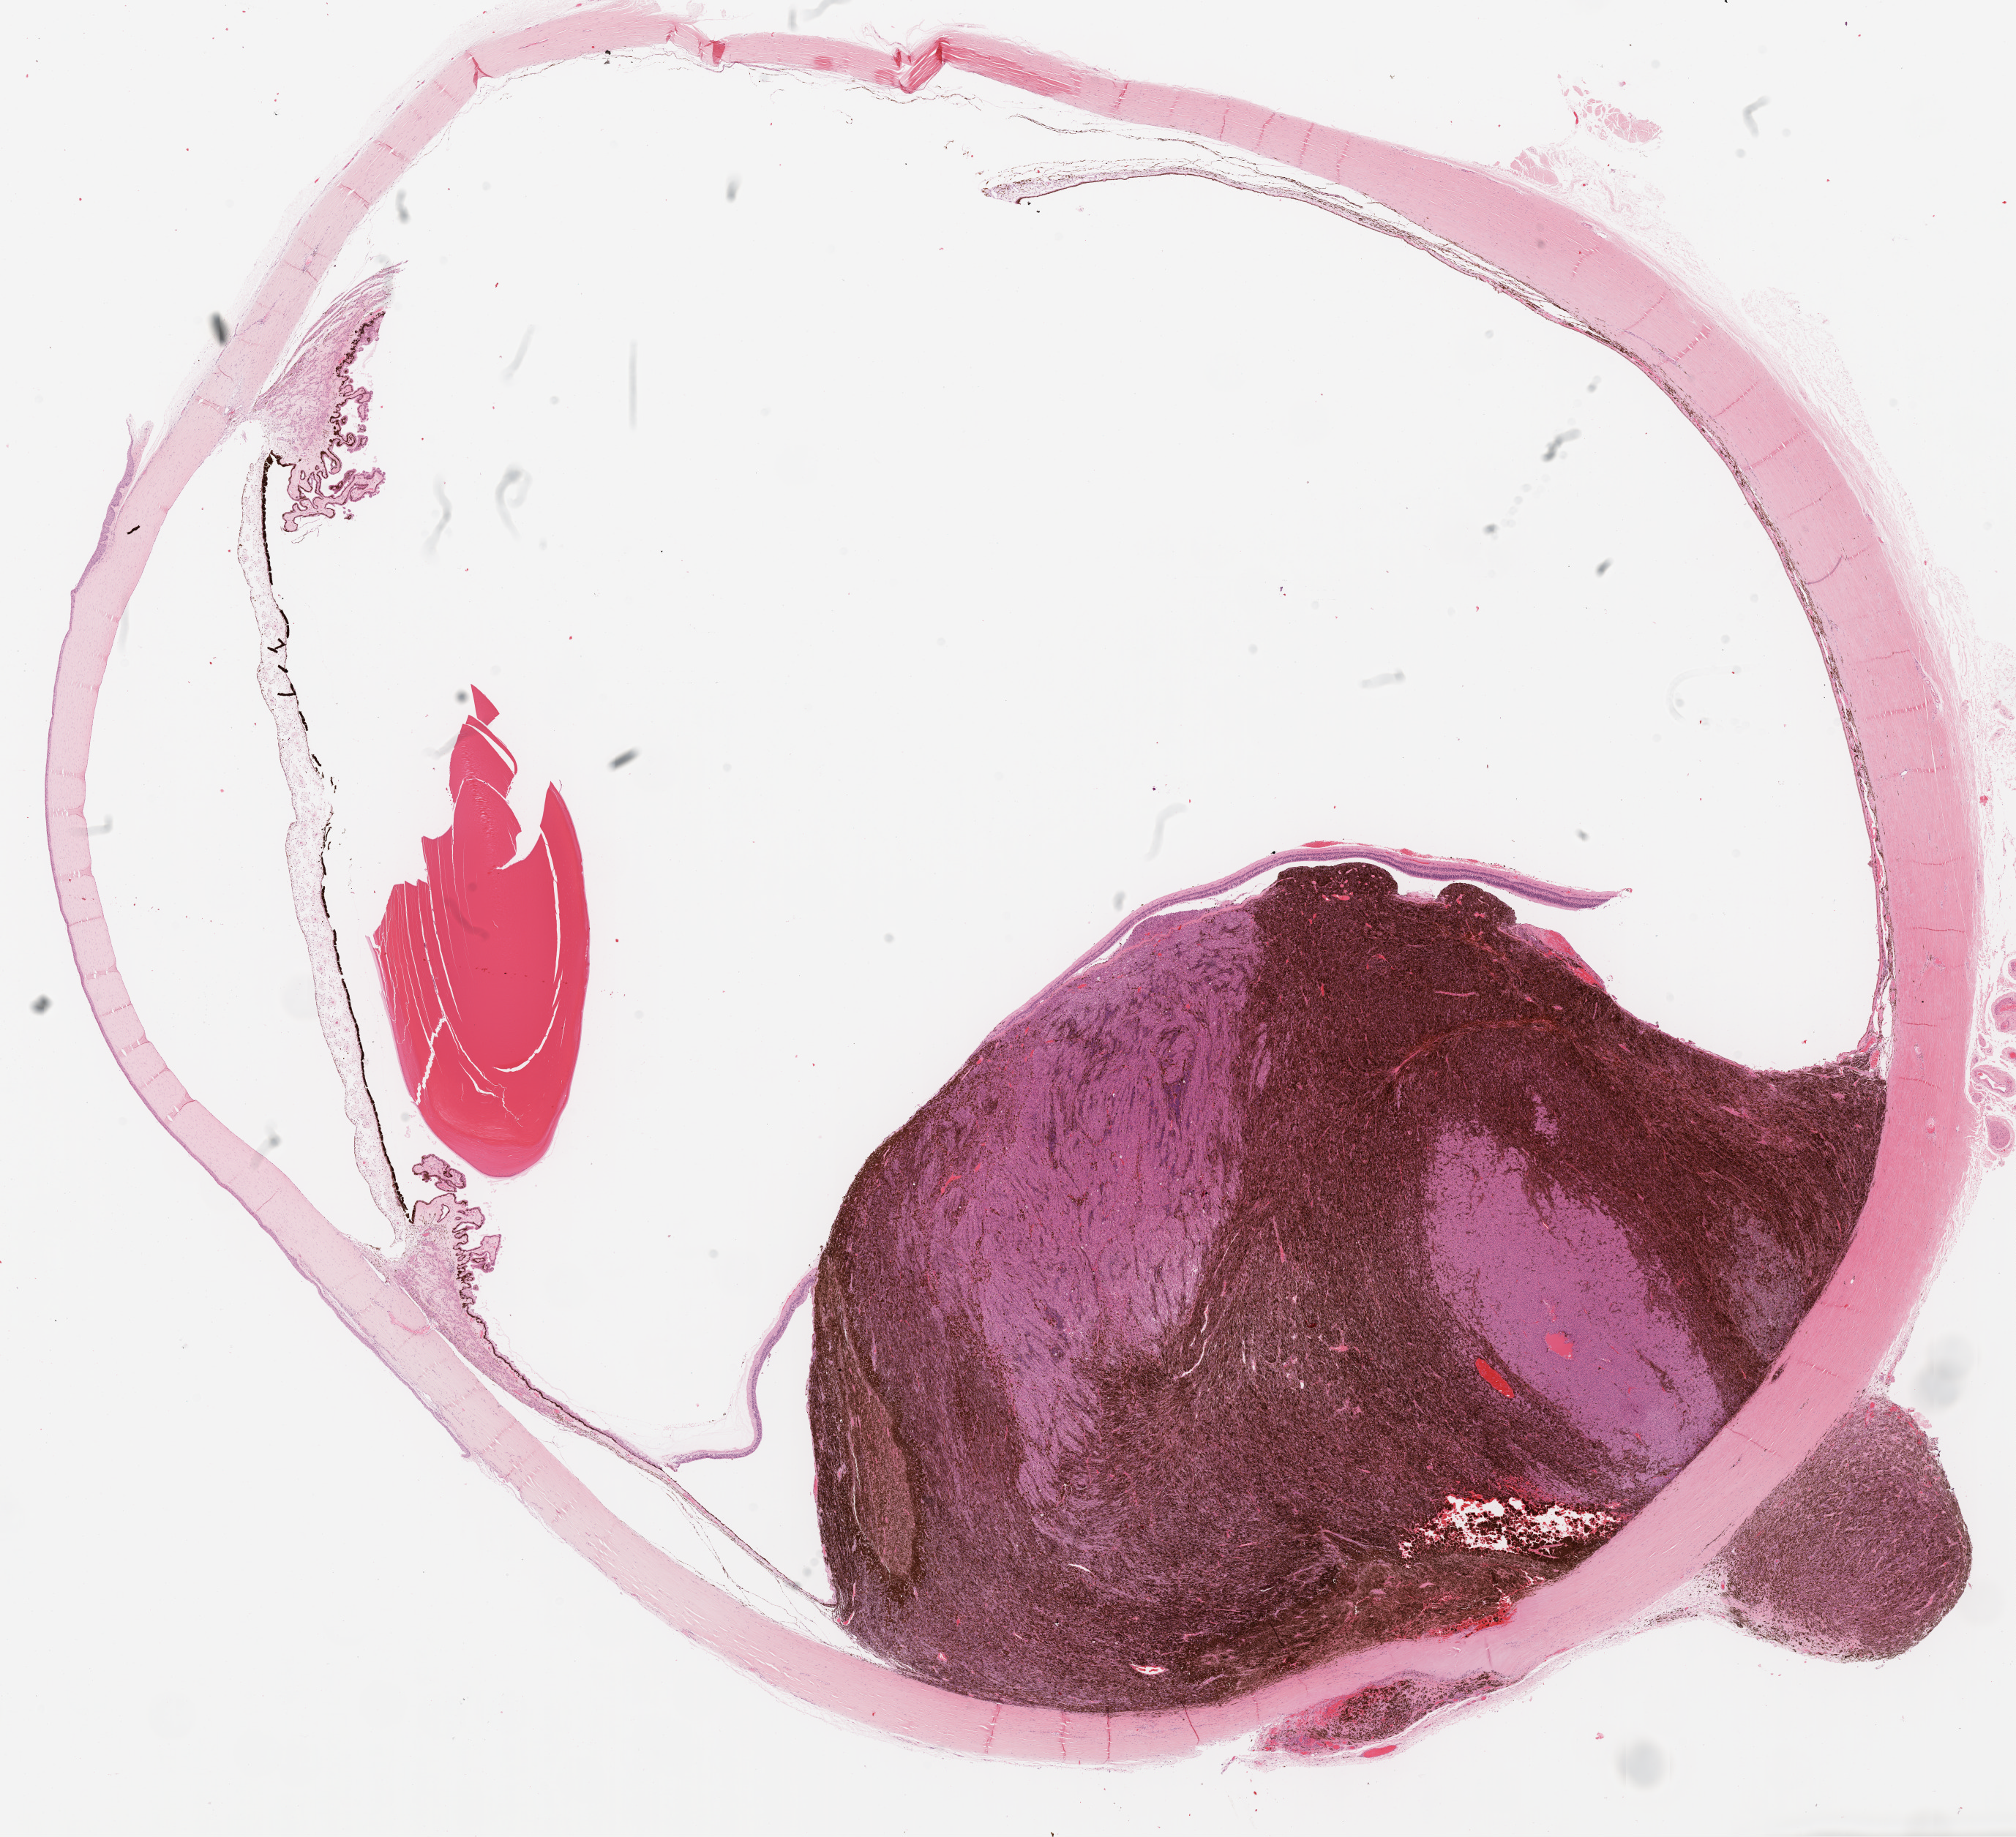
H&E whole-slide image, whole scanned area (about 22.2 x 20.3 mm, from a 20x scan) shown as a low-resolution overview, formalin-fixed paraffin-embedded (FFPE) diagnostic section, primary tumour sample from the uvea. Male patient; age at initial diagnosis 68 years.
Pathologic diagnosis: Mixed epithelioid and spindle cell melanoma. TNM: T3a NX MX. AJCC pathologic stage: IIB (7th edition).